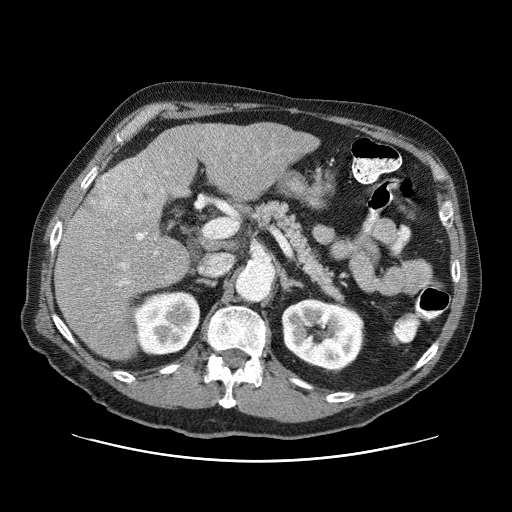
Contrast-enhanced abdominal CT (liver protocol), one axial slice; slice 37 of 87 in the series (ordered by position); 120 kVp; one of 3 acquisitions stored at this slice position; soft-tissue window (W 400 / L 40 HU); 2.5 mm slice thickness; 512 × 512 image matrix, field of view 400 × 400 mm. Case-level facts recorded for this patient, not image findings: diagnosis: hepatocellular carcinoma (patient treated with transarterial chemoembolisation; whether this scan precedes or follows treatment is not stated here); TNM stage (as recorded): Stage-IIIA; Child-Pugh class: A; tumour nodularity: multinodular; tumour size: 6 cm.
Annotated regions visible in this slice (semi-automatically segmented with operator editing):
- liver parenchyma outside the tumour (the mass and vessels are separate outlines, so this box may not span the whole liver): bounding box [x1, y1, x2, y2] px = [54, 122, 318, 360]
- mass: [90, 153, 170, 228]
- liver vessels: [119, 171, 168, 285]